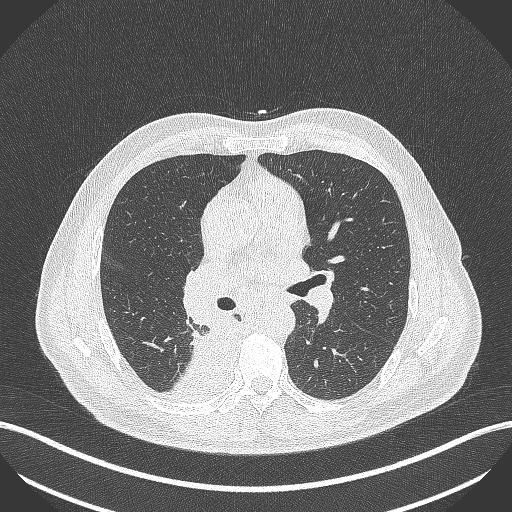
Chest CT, one axial slice; position 264 of 451 along the scan axis; reconstruction kernel B70f; 100 kVp; lung window (W 1500 / L -600 HU); 512 × 512 image matrix. Male patient, age 61 years. From the clinical record (not read from this slice): clinical TNM (as recorded): T1 N0 M0.
Annotated regions visible in this slice (bounding box drawn by a radiologist):
- lung tumour (recorded histology: small cell carcinoma): bounding box (x1, y1, x2, y2) in pixels: (190, 311, 243, 373)